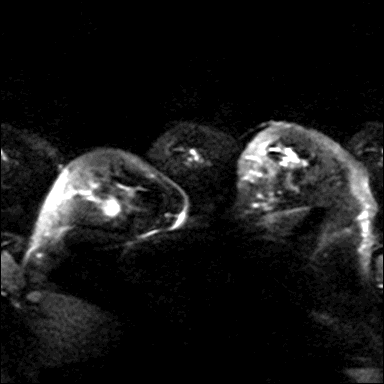
Breast MRI, one axial slice. Slice 26 of 40 in the series (ordered by position). Diffusion-weighted series; image 2 of 4 stored at this slice position (different b-values; order by instance number). 3 T. 4 mm slice thickness. 384 × 384 image matrix, field of view 320 × 320 mm. Female patient.
Outlined on this slice (outlined manually by an expert reader):
- tumour on diffusion-weighted imaging: bounding box [x1, y1, x2, y2] px = [287, 150, 294, 160]